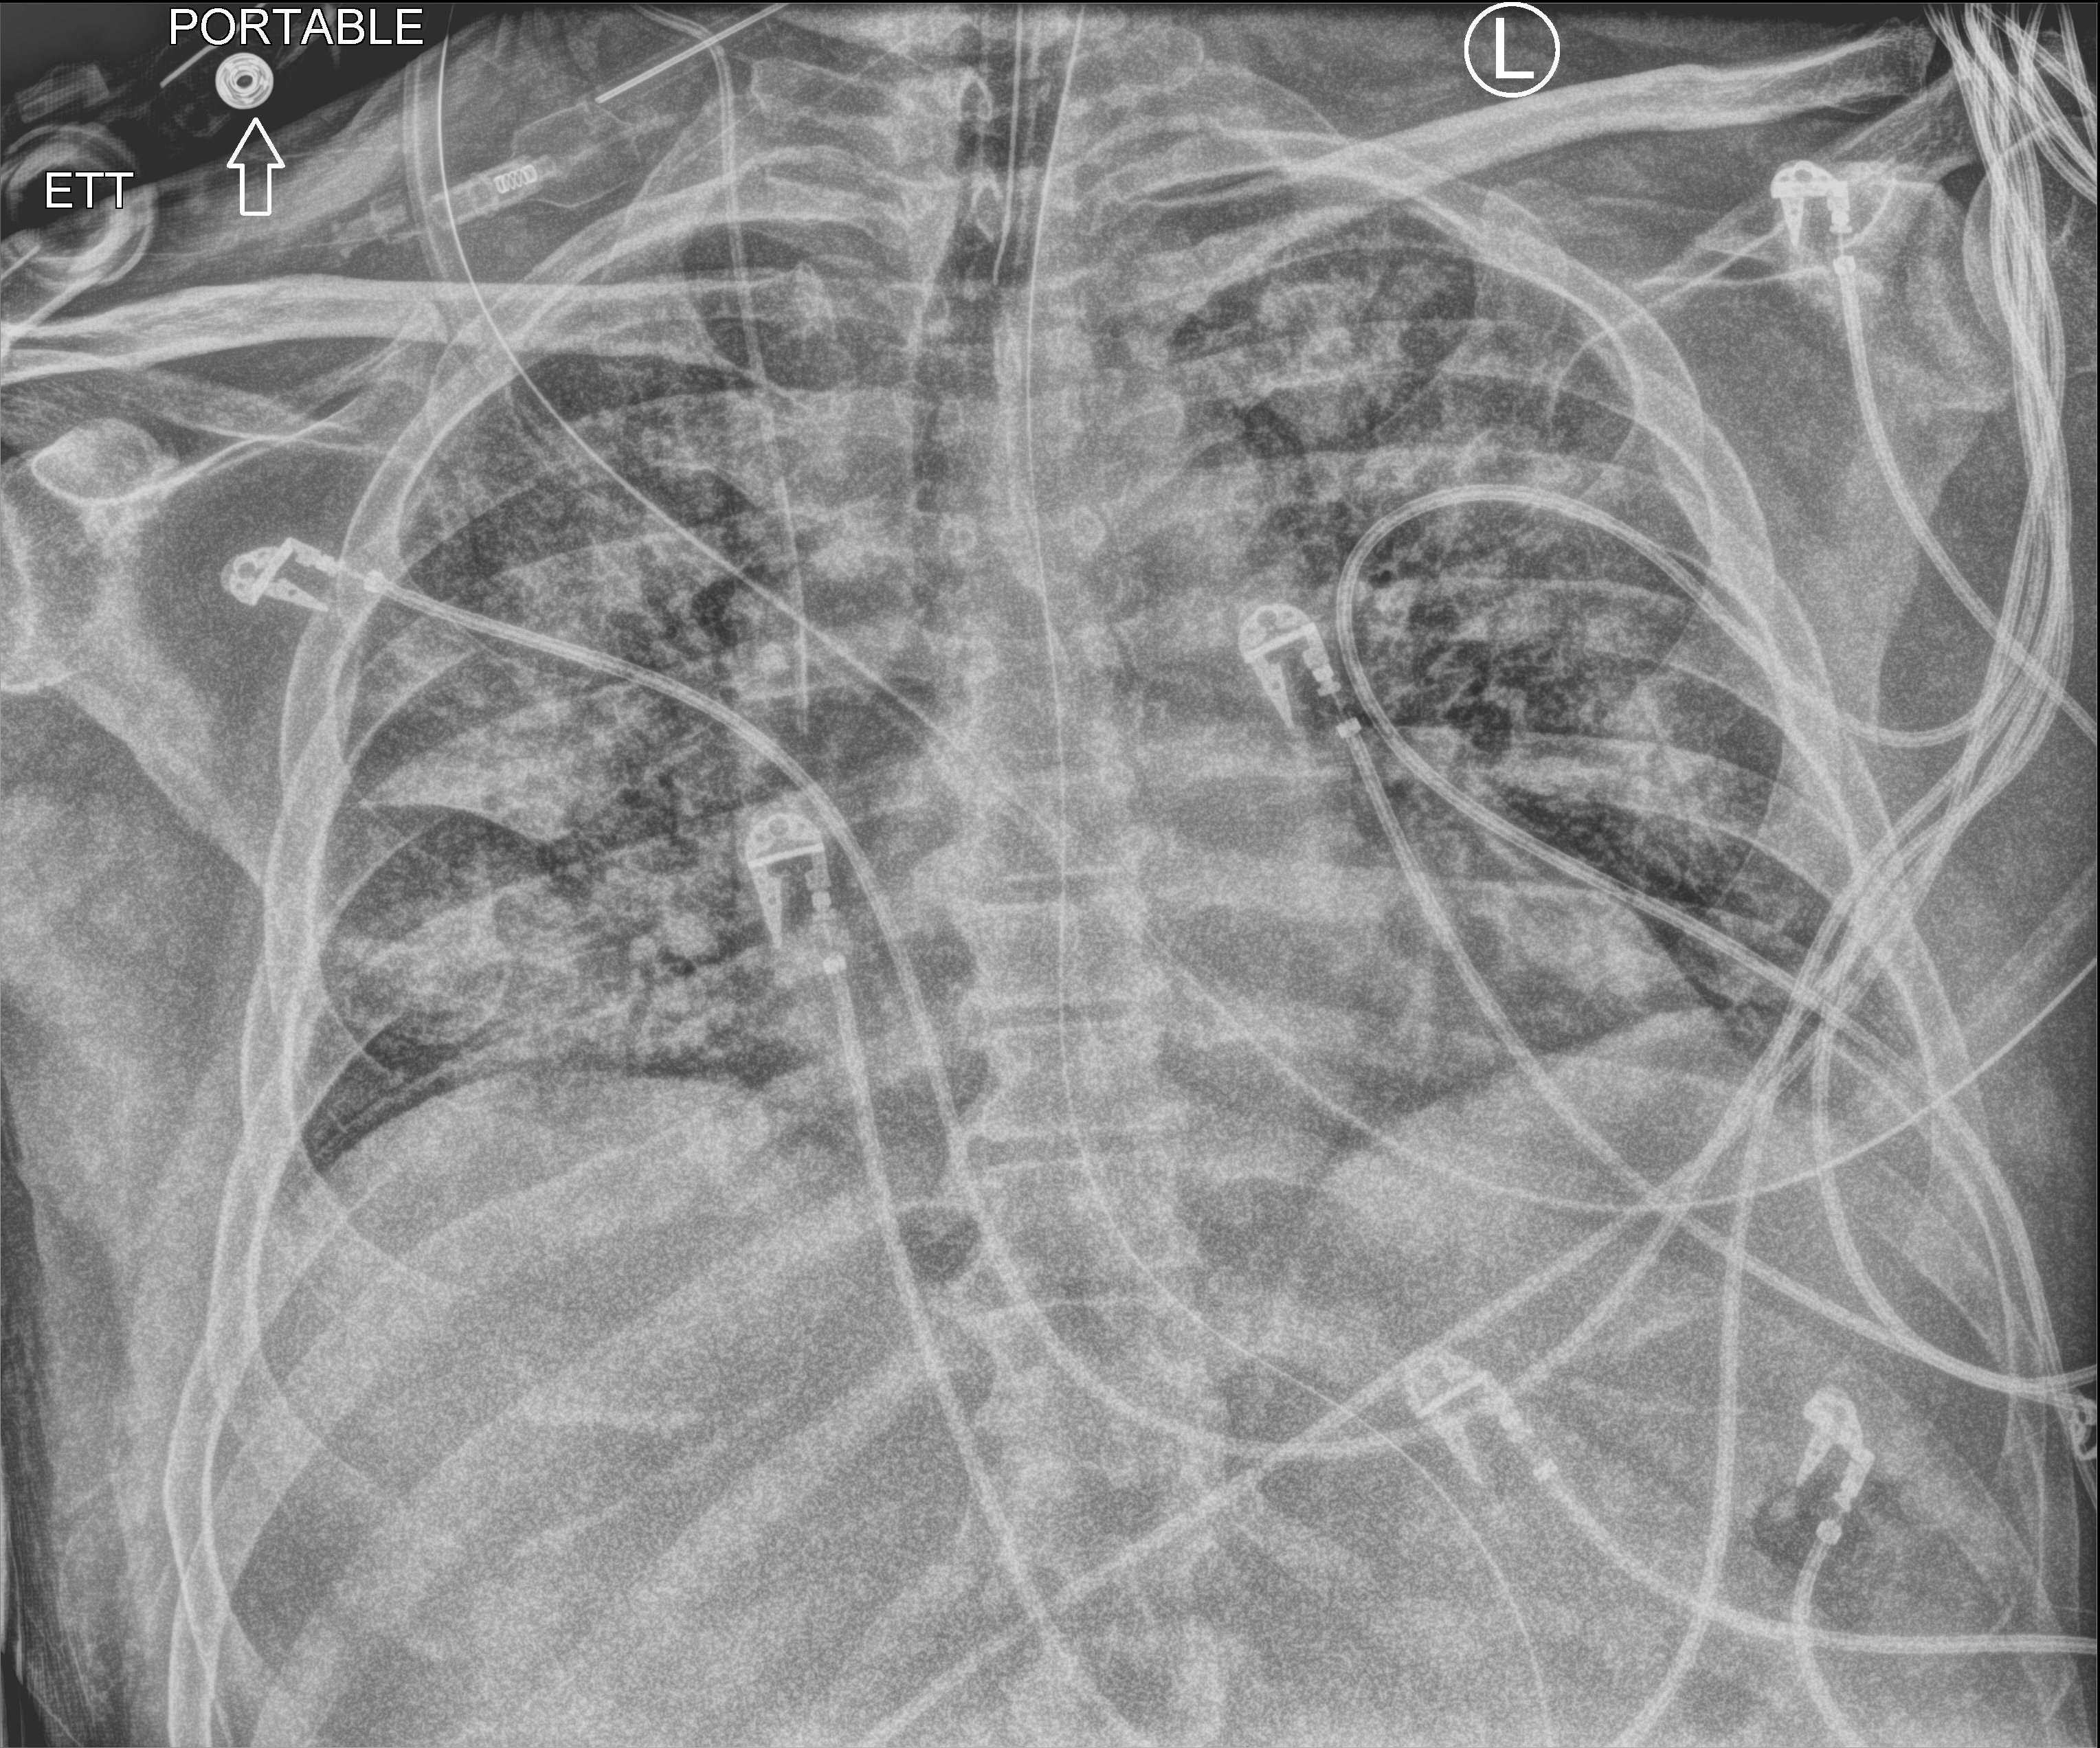
Chest X-ray (portable). Male patient hospitalised with COVID-19, age 60–74 years.
Hospital-stay facts (about this admission, not read from this image; timing relative to this image not recorded): admitted to intensive care during this hospital stay: yes; length of hospital stay: 33 days; mechanically ventilated during this hospital stay: yes.